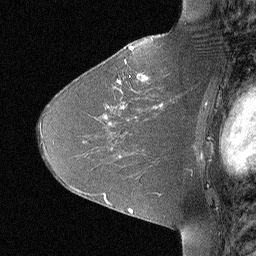
Breast MRI (dynamic contrast-enhanced), one sagittal slice. Slice 44 of 64 in the series (ordered by position). Dynamic contrast-enhanced study with each time point stored as its own series, time point 2 of 3 at this slice position (early post-contrast, ordered by acquisition time). 1.5 T. TE 4 ms, TR 30 ms. 256 × 256 image matrix. Patient: female, 46 years. From the clinical record (not read from this slice): setting: breast cancer imaged before/during neoadjuvant chemotherapy; receptor status: HR-positive, HER2-negative.
Annotated regions visible in this slice (semi-automatically segmented with operator editing):
- analysis volume of interest (the breast-tissue region the enhancement analysis was run in; not a lesion): box from (x=106, y=43) to (x=184, y=119) px
- tumour enhancement mask (voxels above the 90 % enhancement threshold inside the analysis volume of interest): (x=117, y=47)–(x=133, y=83)